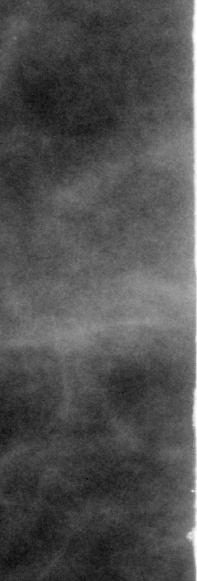
Crop from a digitized film mammogram around one marked abnormality, right breast, CC view, BI-RADS breast density category 2 (scale 1–4).
- Marked abnormality: mass, shape irregular, margins ill defined; BI-RADS assessment category 4; pathology (as recorded): benign.